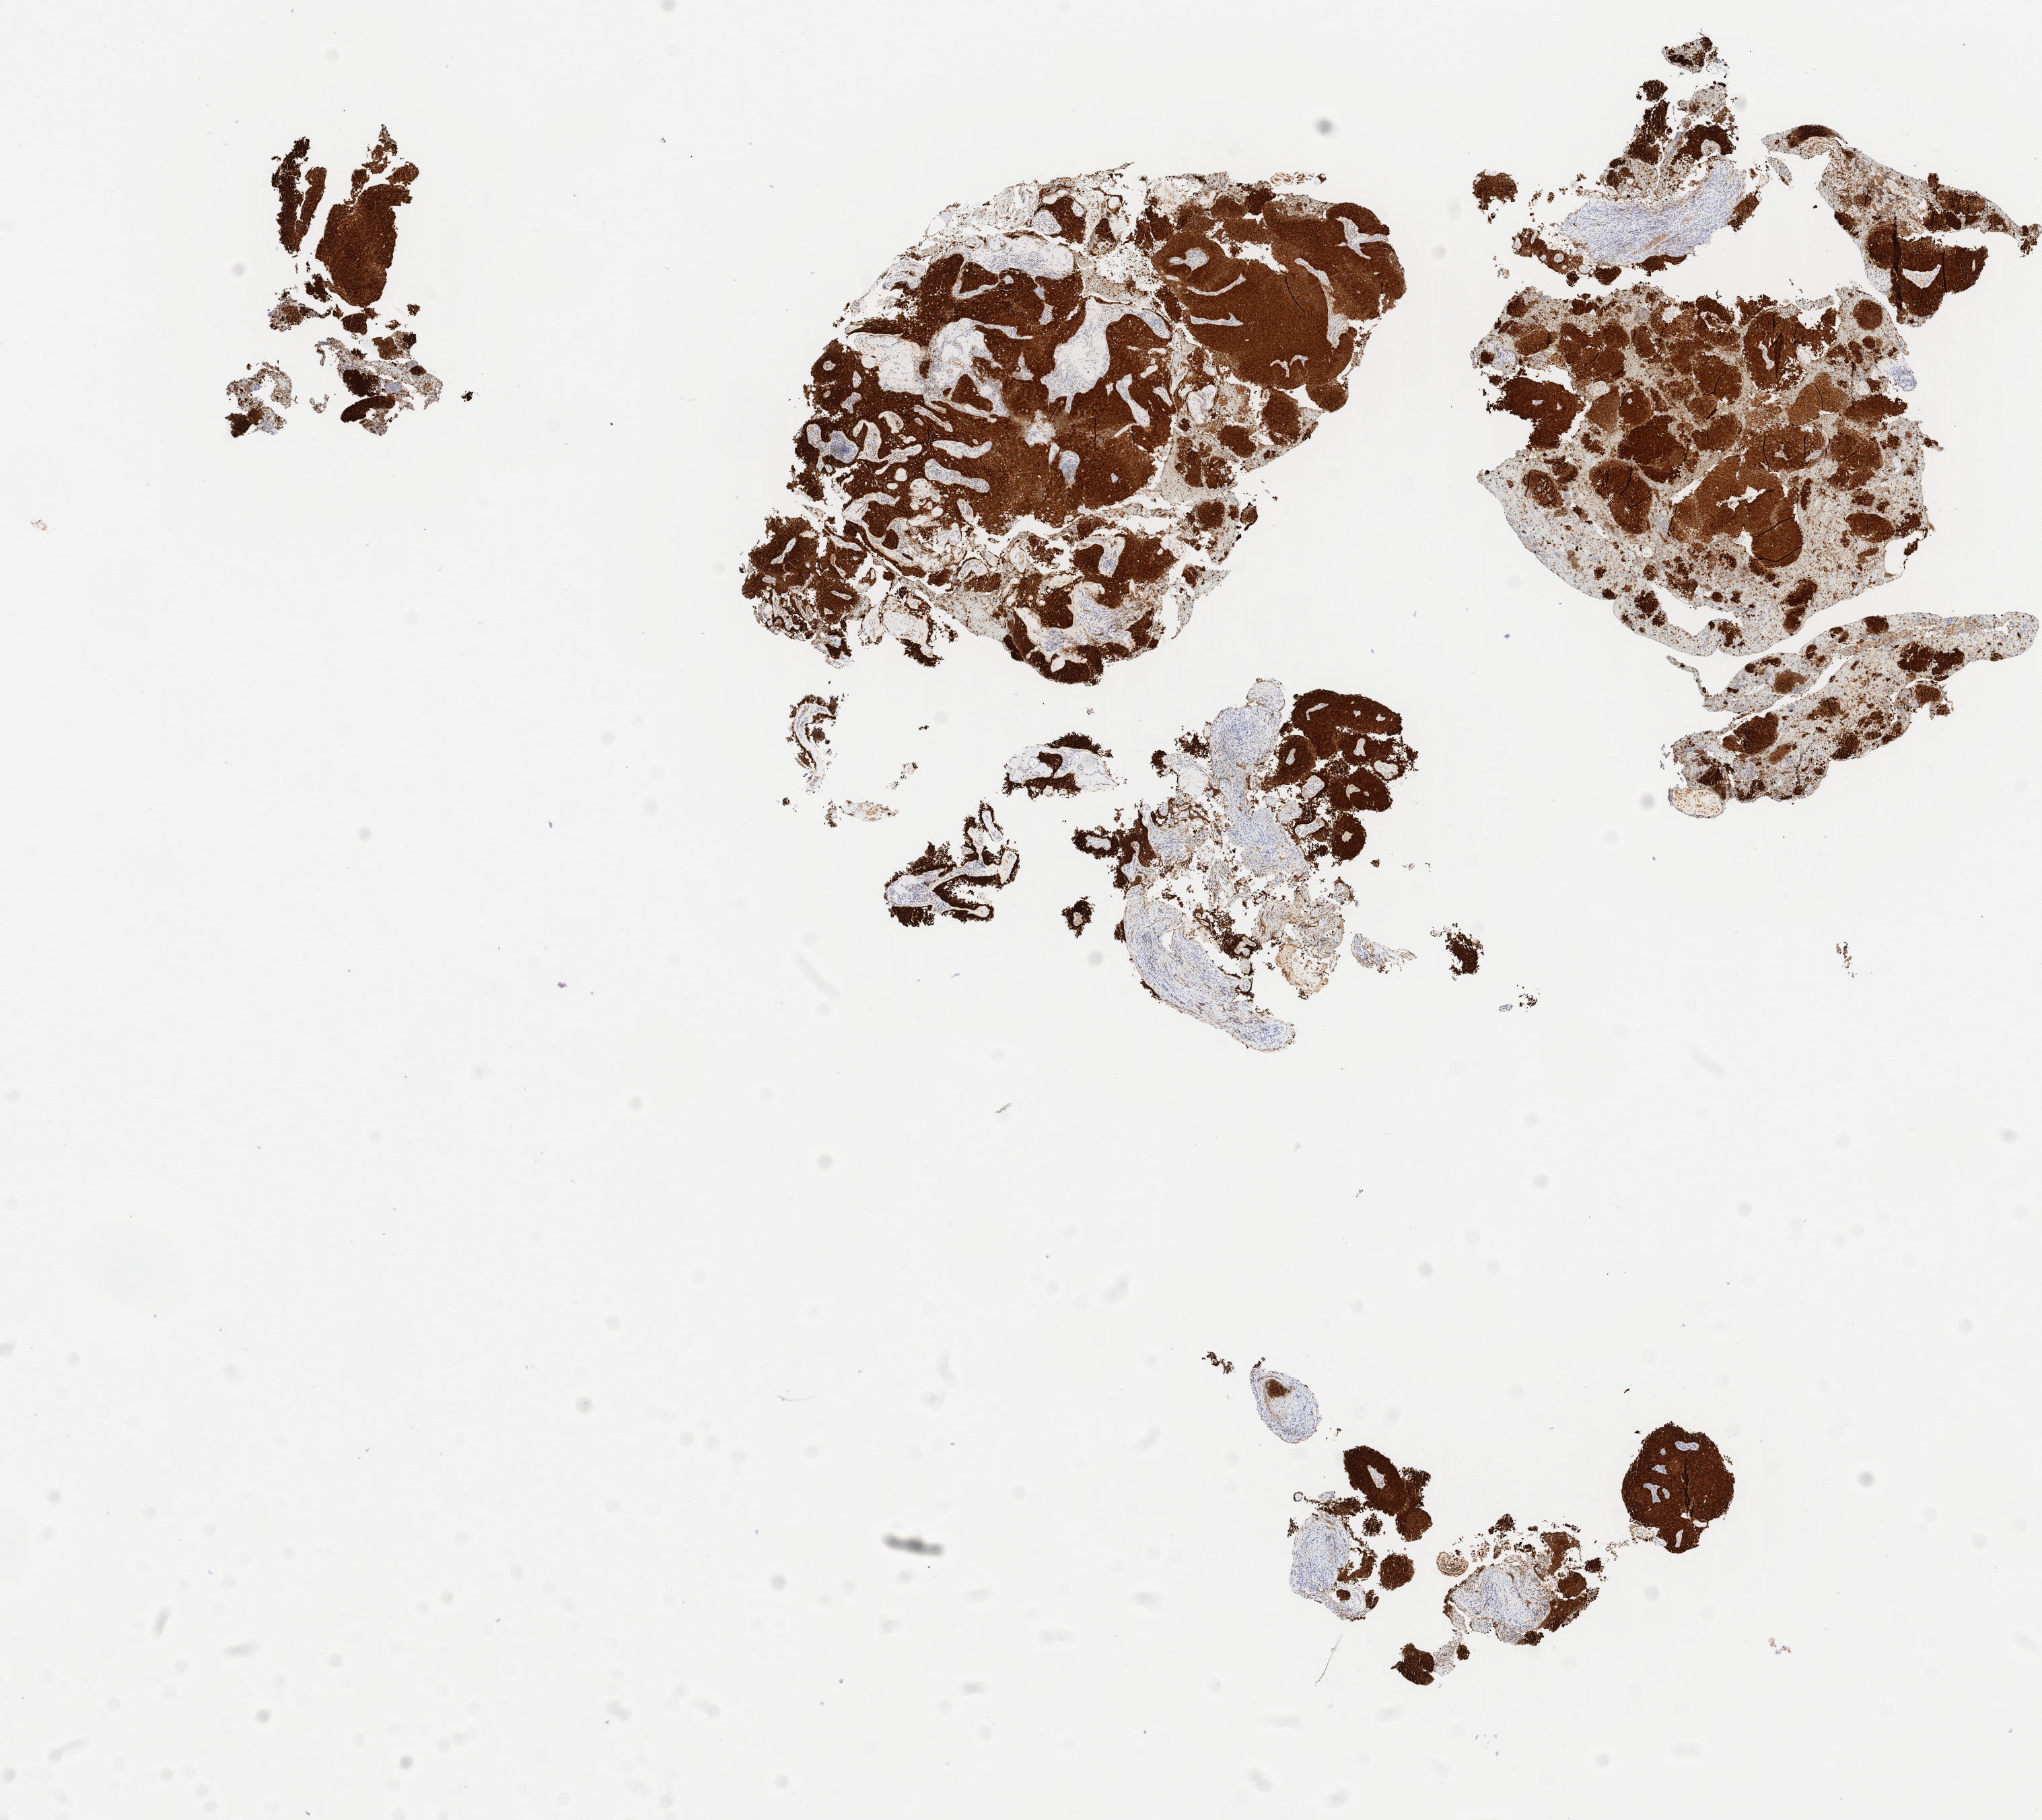
Immunohistochemistry (IHC) whole-slide image stained for p16 (p16INK4a) — a low-resolution overview of the entire scanned area, about 12.1 x 10.8 mm; tumor tissue; site: cervix. Patient: female, 44 years old.
Diagnosis: Squamous cell carcinoma, large cell, nonkeratinizing, NOS.